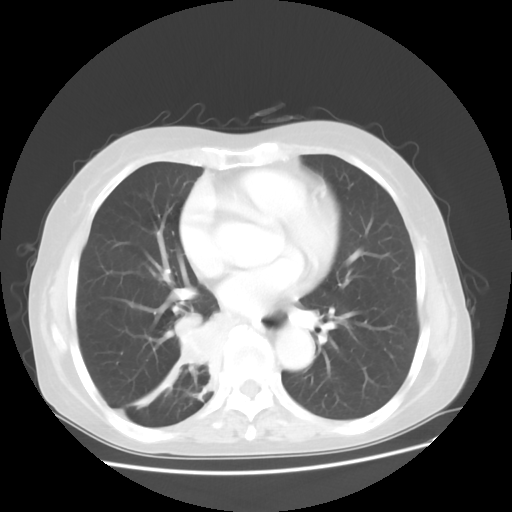
Chest CT, one axial slice. Slice 19 of 48 in the series (ordered by position). Reconstruction kernel STANDARD. 120 kVp. Lung window (W 1500 / L -600 HU). 512 × 512 image matrix, field of view 360 × 360 mm. Patient: female, 63 years. From the clinical record (not read from this slice): clinical TNM (as recorded): T2 N3 M1b; histopathological grade: G3.
Annotated regions visible in this slice (bounding box drawn by a radiologist):
- lung tumour (recorded histology: small cell carcinoma): bounding box (x1, y1, x2, y2) in pixels: (165, 310, 228, 376)